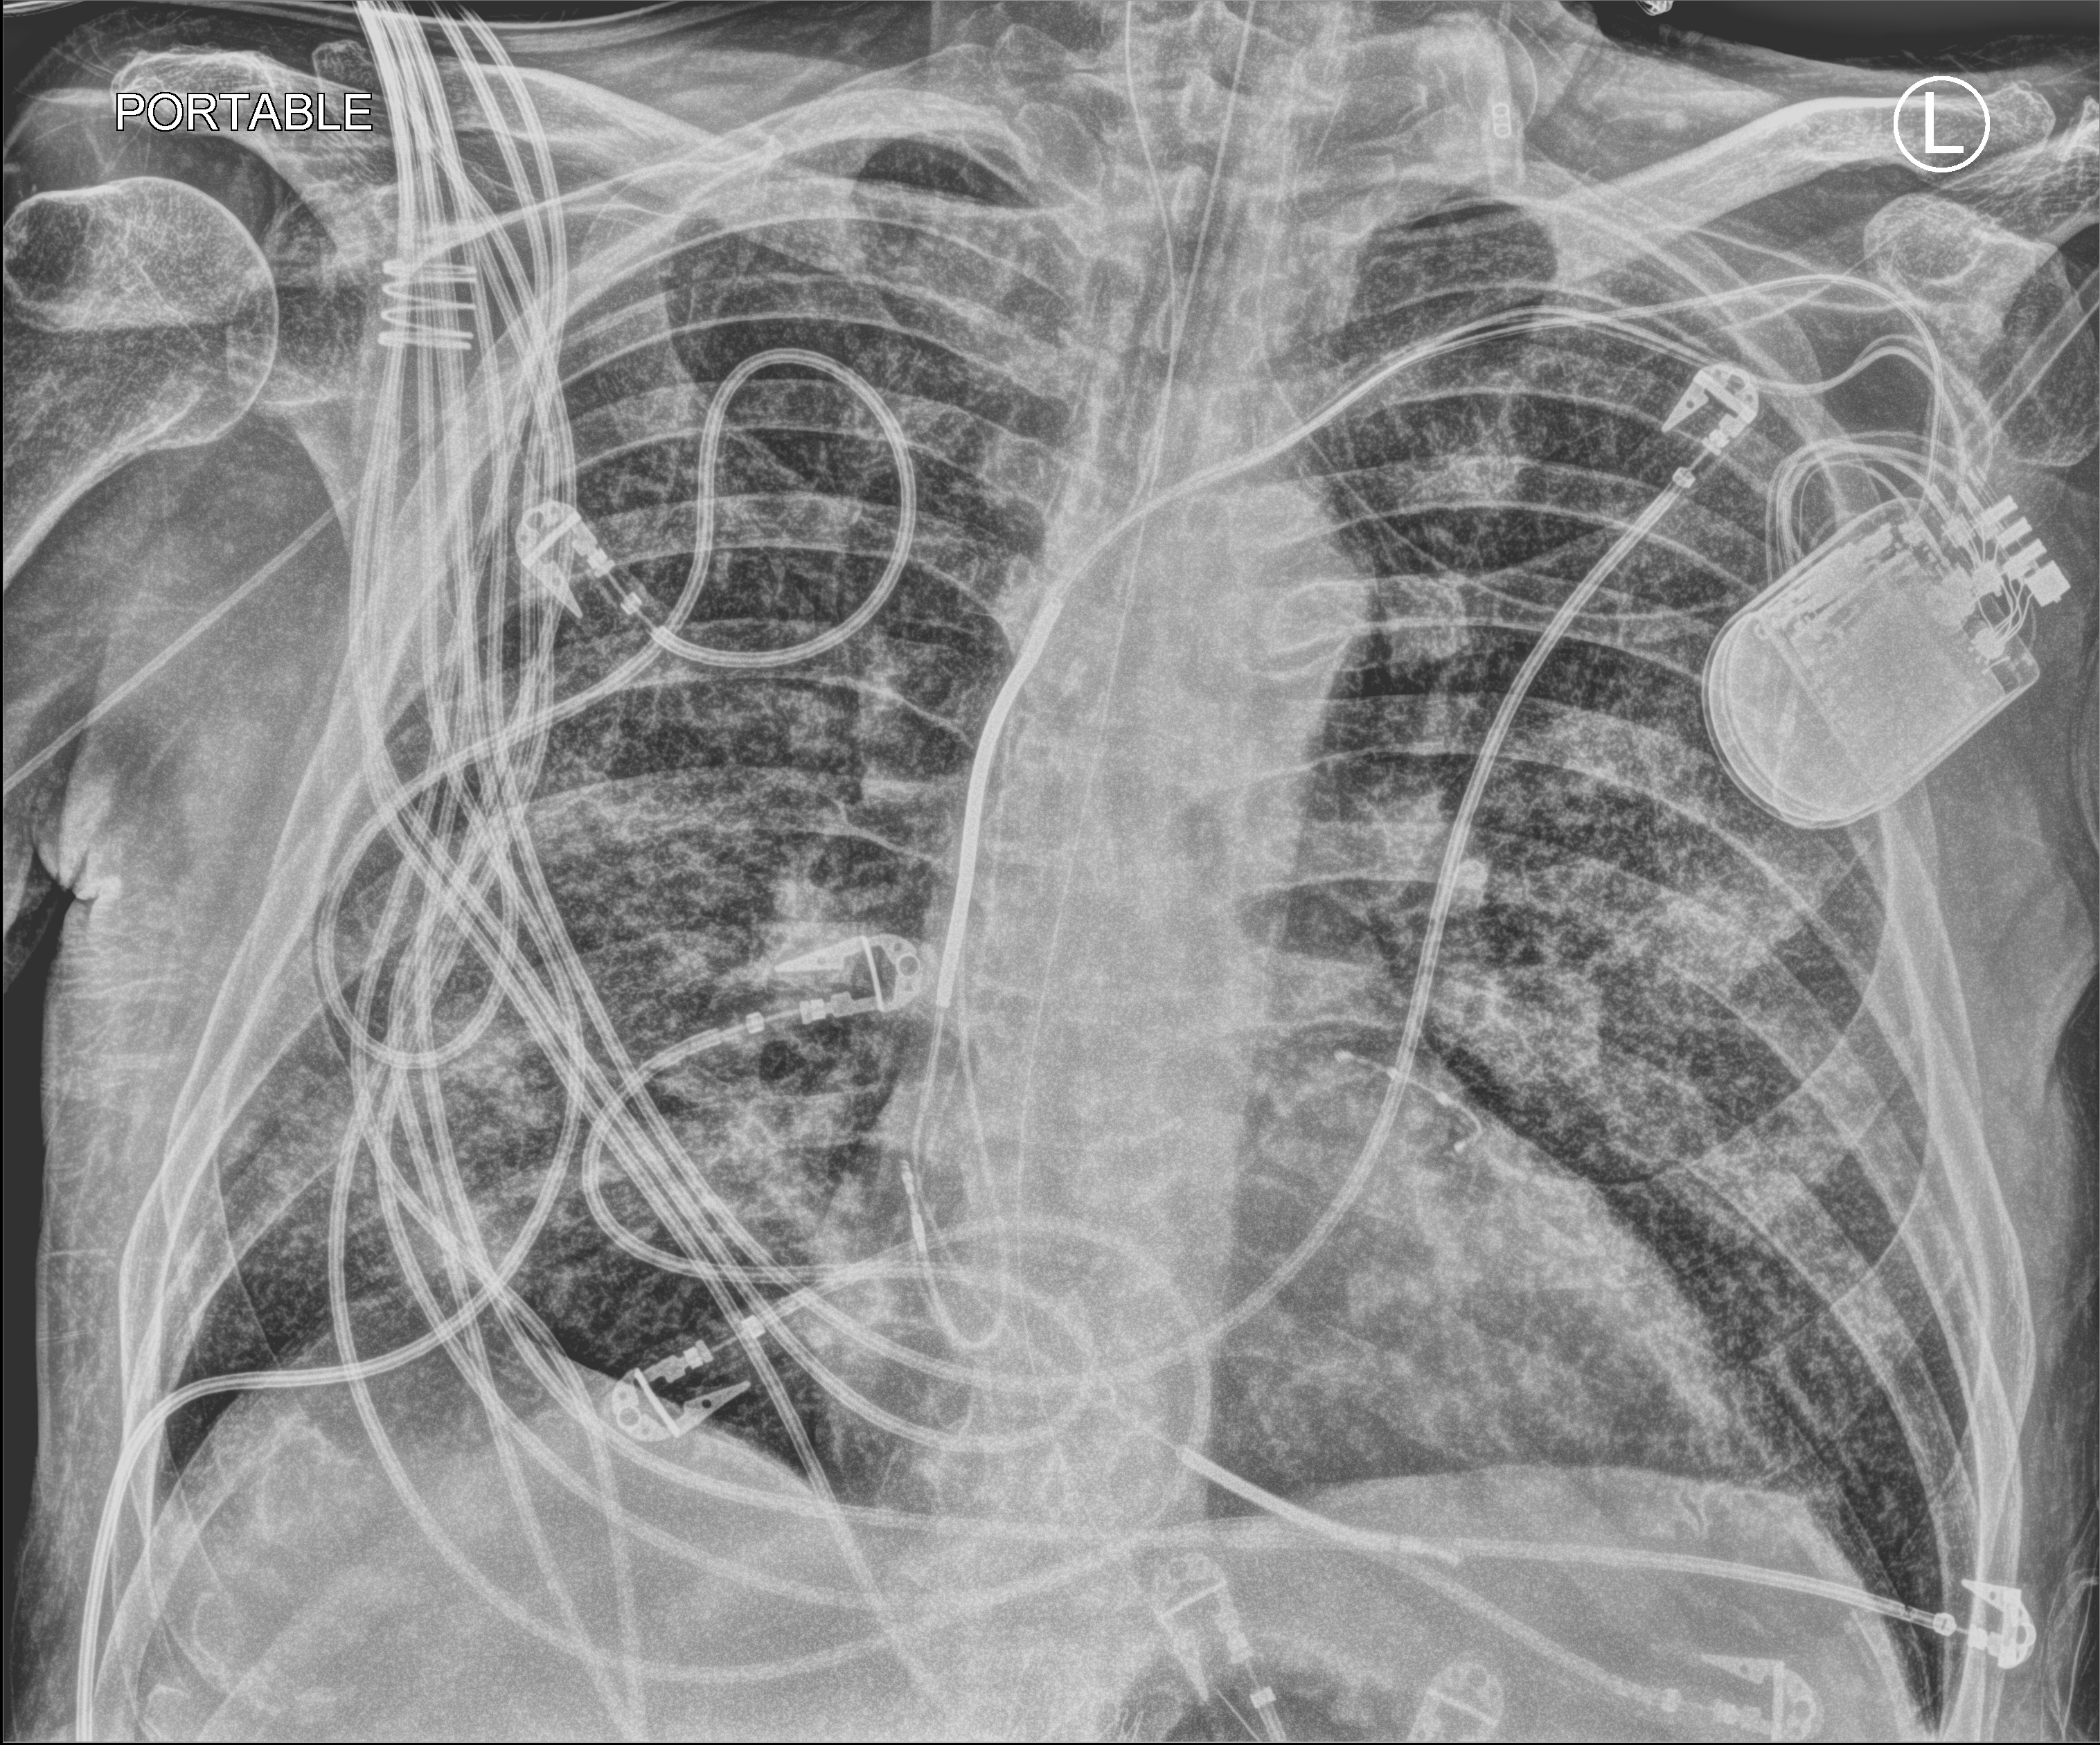
Bedside chest radiograph (computed radiography). Male patient hospitalised with COVID-19, age 60–74 years.
Hospital-stay facts (about this admission, not read from this image; timing relative to this image not recorded):
- hypertension (admission record): yes
- mechanically ventilated during this hospital stay: yes
- diabetes (admission record): yes